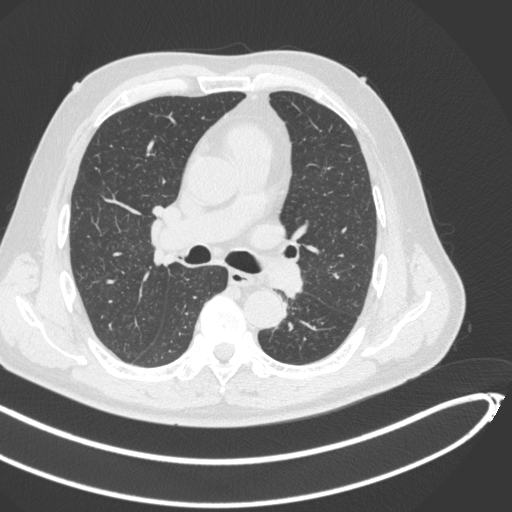
Chest CT, one axial slice; lung window (W 1500 / L -600 HU); 512 × 512 image matrix, field of view 400 × 400 mm. Male patient, age 64 years. From the clinical record (not read from this slice): clinical TNM (as recorded): T1c N0 M0; histopathological grade: G2.
Annotated regions visible in this slice (bounding box drawn by a radiologist):
- lung tumour (recorded histology: squamous cell carcinoma): box from (x=259, y=246) to (x=305, y=300) px